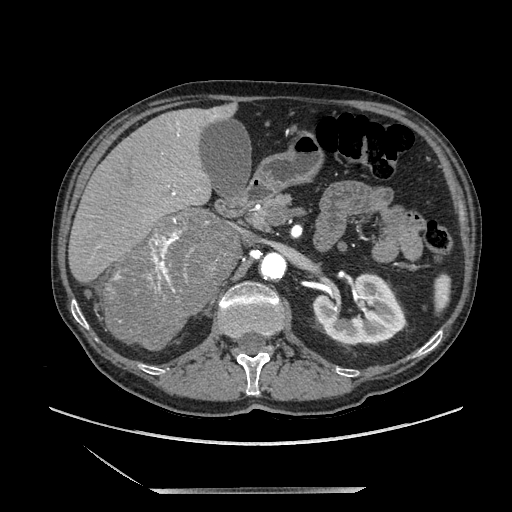
Contrast-enhanced abdominal CT, one axial slice; slice 113 of 243 in the series (ordered by position); soft-tissue window (W 400 / L 40 HU); 1.25 mm slice thickness; 512 × 512 image matrix, field of view 420 × 420 mm. Male patient. From the clinical record (not read from this slice): diagnosis: adrenocortical carcinoma; tumour side: right adrenal; tumour size at pathology: 16 cm; Ki-67 index: 17 %; stage (as recorded): 3.
Outlined on this slice (semi-automatically segmented with operator editing):
- mass: bounding box <107,209,238,346> (left, top, right, bottom; pixels)